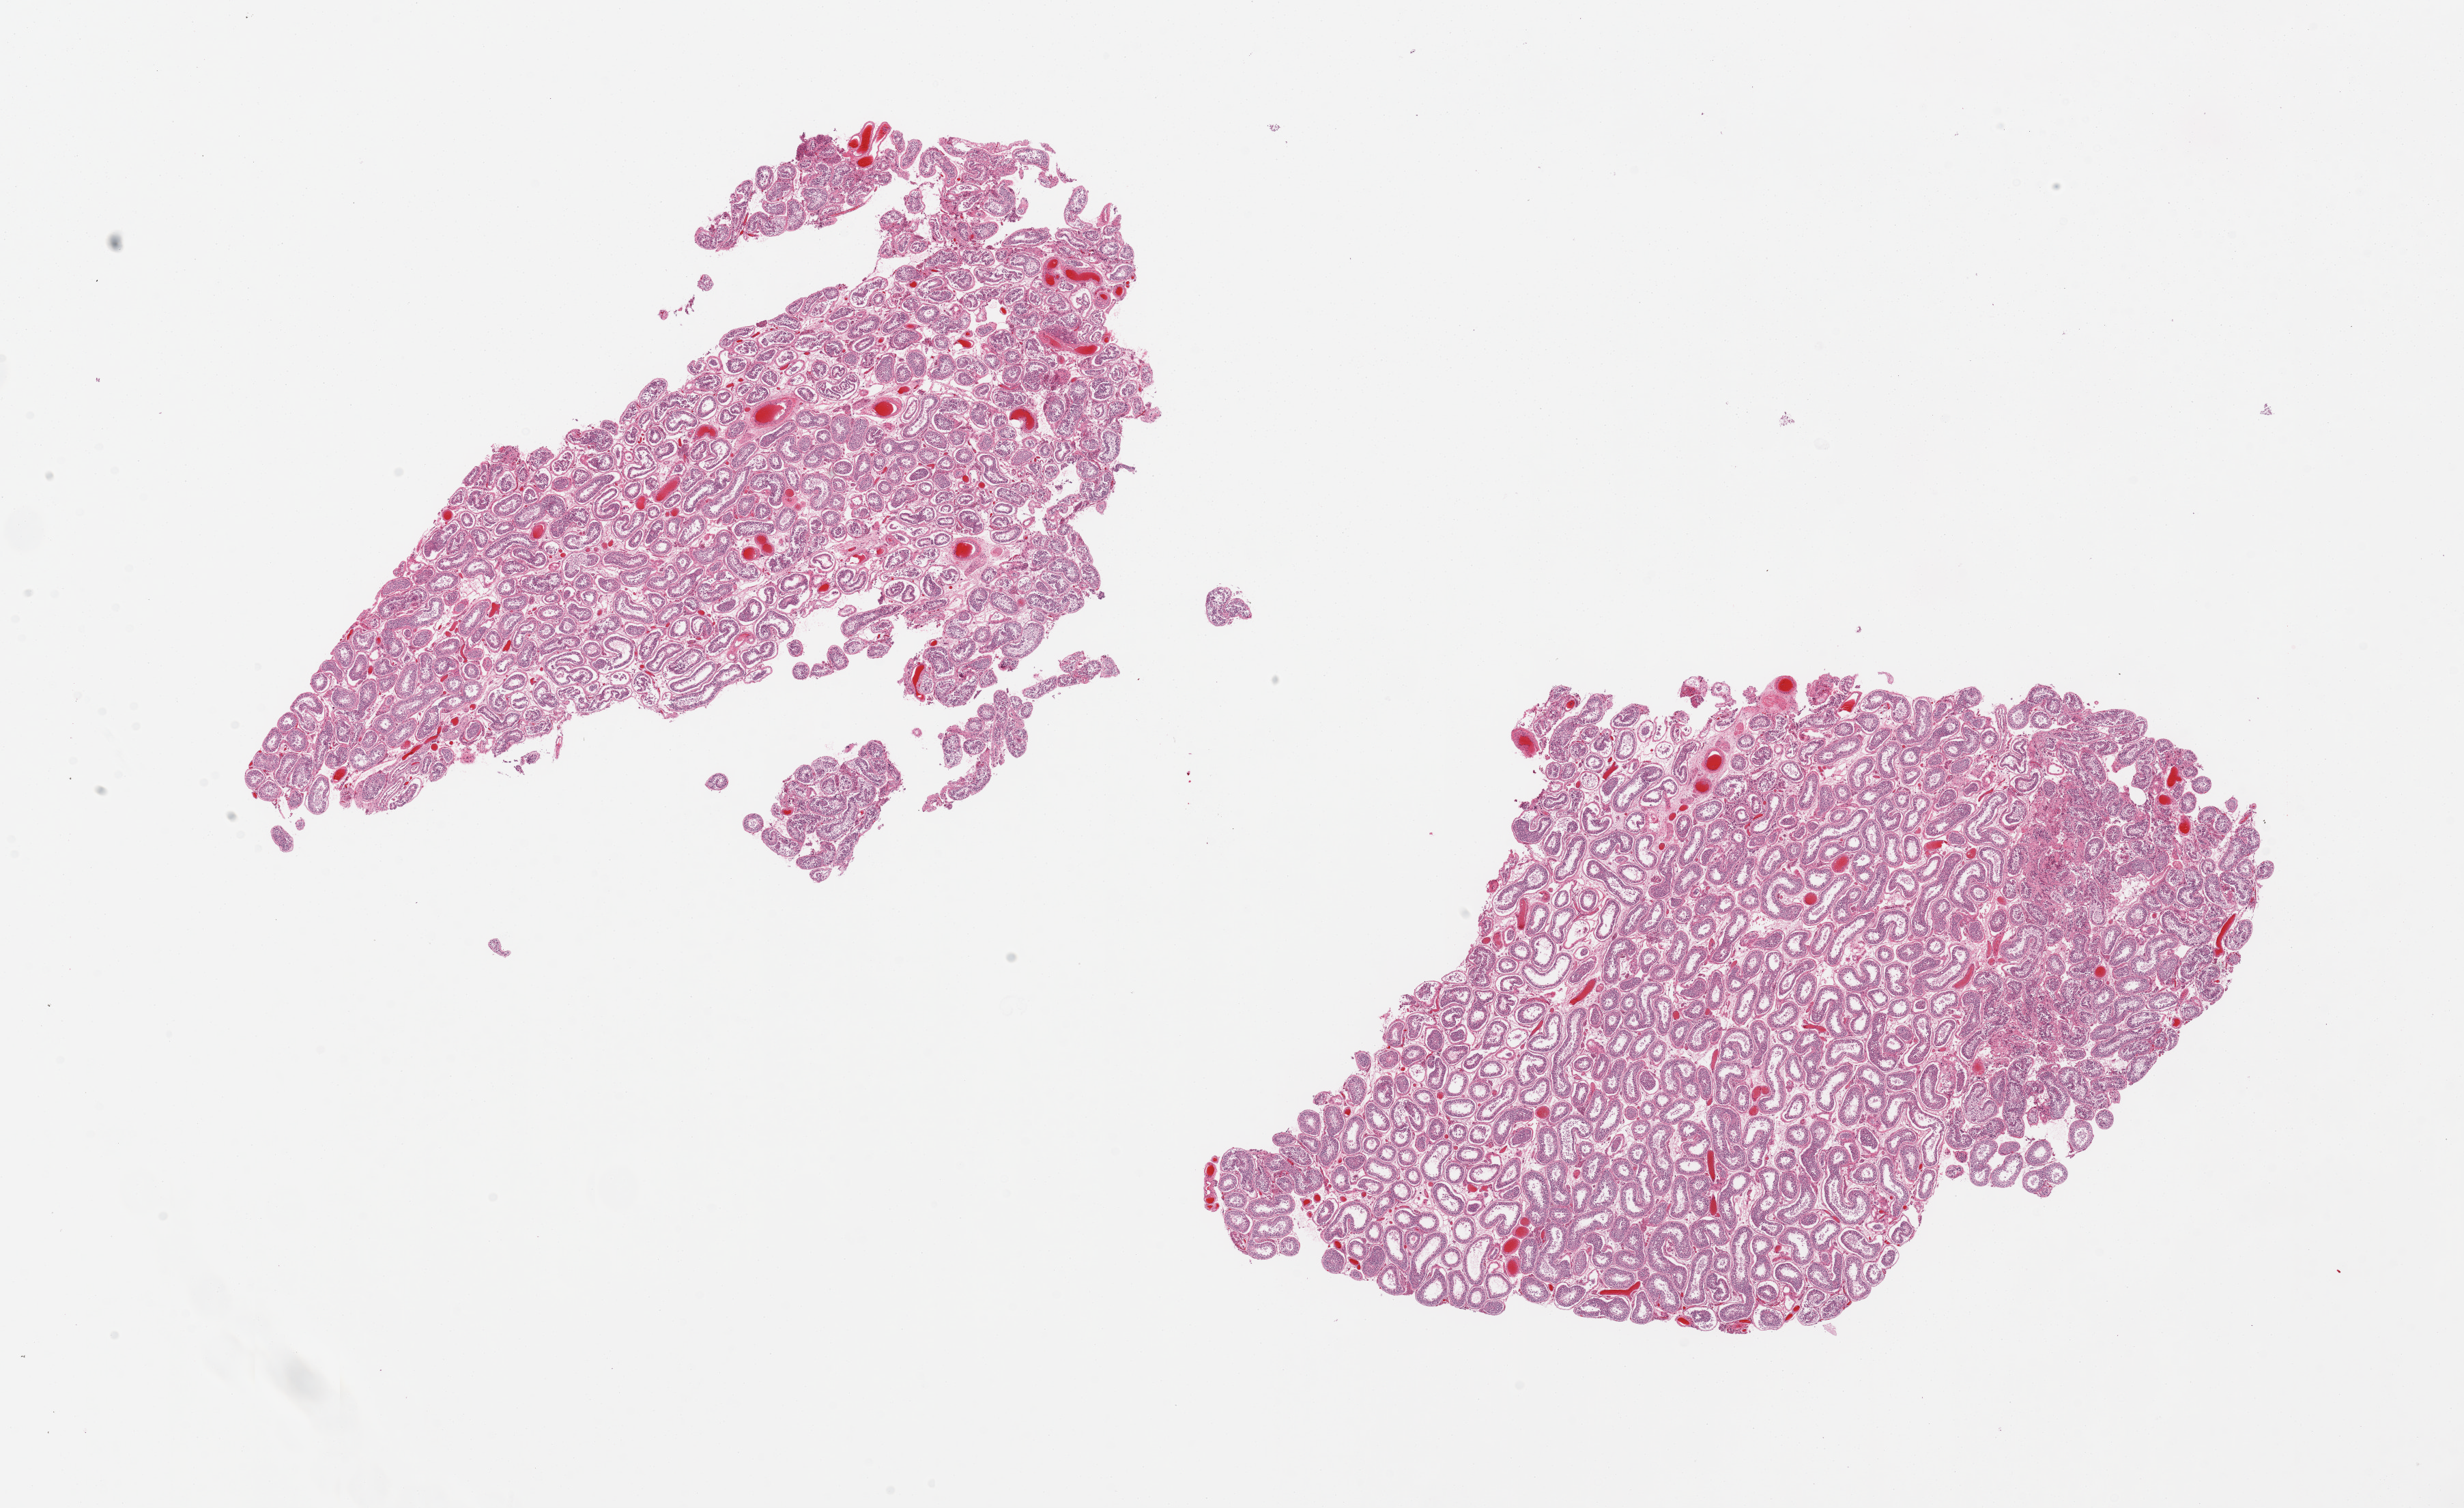
Digitized haematoxylin and eosin-stained section, brightfield — shown as a low-resolution overview of the whole scanned area (about 28.5 x 17.5 mm), PAXgene-fixed paraffin-embedded (PFPE) section, sampled site (target tissue): testis, donor tissue sample.
Pathologist's review note for this sample: 2 pieces, spermatogenesis present.